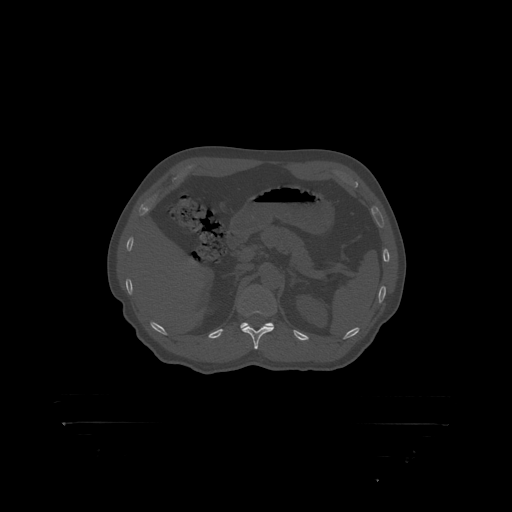
CT including the spine, one axial slice. Position 343 of 399 along the scan axis. Bone window (W 1800 / L 400 HU). 512 × 512 image matrix, field of view 650 × 650 mm. Male patient, age 46 years. Case-level facts recorded for this patient, not image findings: primary cancer: skin.
Outlined on this slice (semi-automatically segmented with operator editing):
- T12 vertebra: bounding box [x1, y1, x2, y2] px = [247, 311, 273, 316]